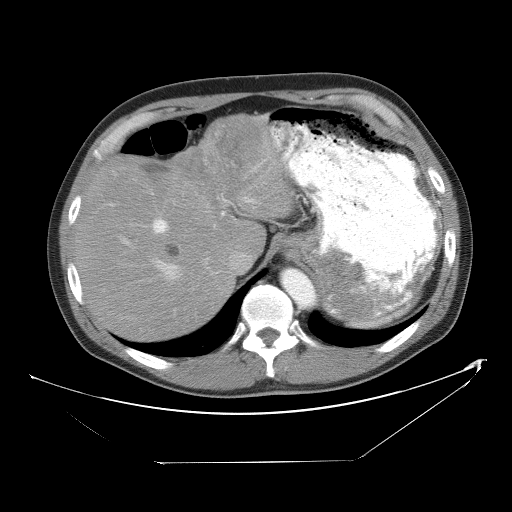
Contrast-enhanced abdominal CT, one axial slice. Slice 39 of 53 in the series (ordered by position). 120 kVp. Soft-tissue window (W 400 / L 40 HU). 512 × 512 image matrix, field of view 438 × 438 mm. Male patient, age 59 years. Case-level facts recorded for this patient, not image findings: diagnosis: colorectal cancer liver metastases, imaged before liver resection; multiple liver metastases: yes; largest metastasis: 8.5 cm; disease in both lobes: no.
Structures marked on this image (manually delineated by an expert):
- hepatic veins: bounding box [x1, y1, x2, y2] px = [125, 241, 182, 280]
- liver: [76, 119, 290, 341]
- planned liver remnant (the part of the liver to remain after resection): [76, 160, 233, 341]
- portal vein (with intrahepatic branches): [151, 193, 256, 235]
- liver metastasis: [165, 242, 182, 259]
- liver metastasis: [221, 134, 247, 166]